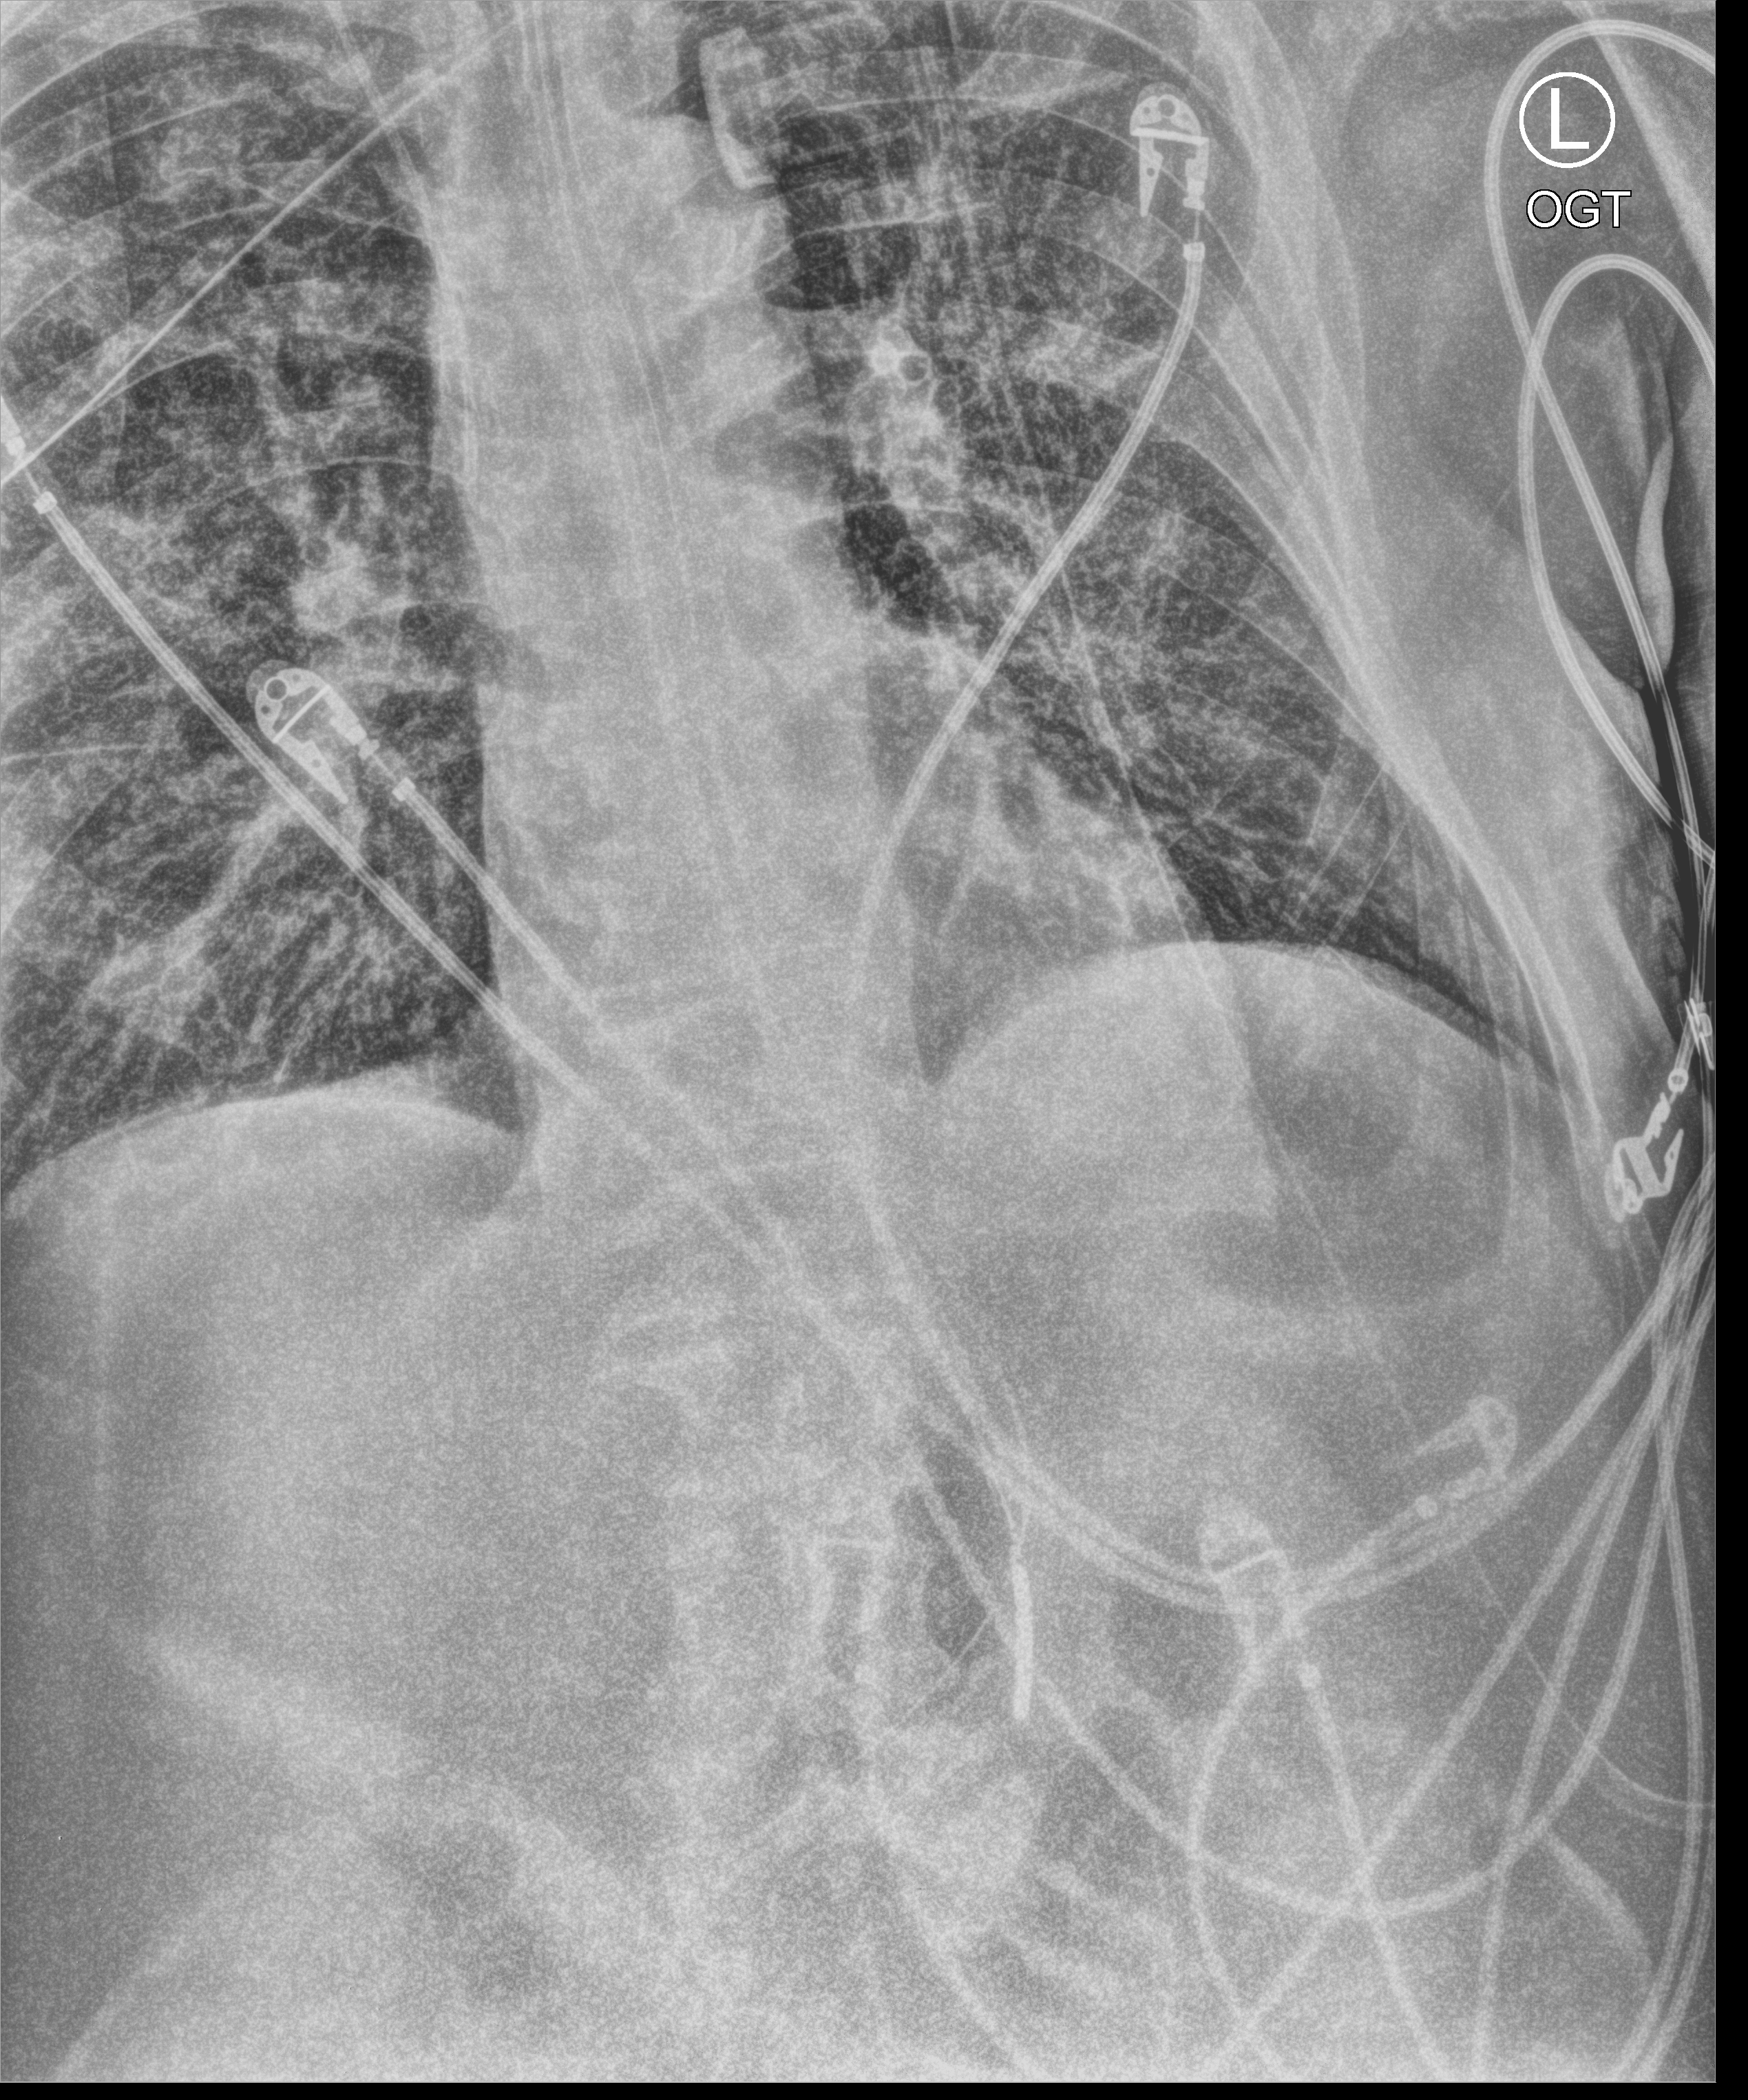
Portable chest radiograph, anteroposterior (AP) projection. Male patient hospitalised with COVID-19, age 75–90 years.
From the hospital-stay record, not from the radiograph (when in the stay this image was taken is not recorded): smoking status (admission record): former; length of hospital stay: 26 days; admitted to intensive care during this hospital stay: yes.